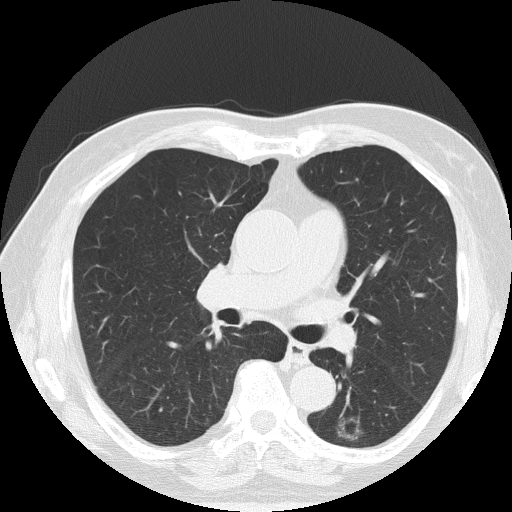
Axial slice from a low-dose chest CT screening exam, baseline screening round, lung window (W 1500 / L -600 HU), 2 mm slice thickness, slice 71 of 145 in the series. Male, age 71 years at enrolment. Former smoker at enrolment.
• Expert-annotated lung lesion, bounding box <320,408,377,453> (left, top, right, bottom; pixels).
• Screening reader's record for this exam: no non-calcified nodule ≥4 mm recorded.